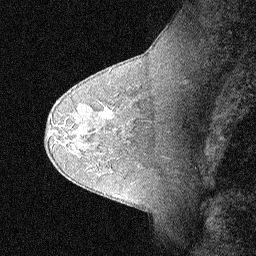
Breast MRI (dynamic contrast-enhanced), one sagittal slice; slice 46 of 64 in the series (ordered by position); dynamic contrast-enhanced study with each time point stored as its own series, time point 2 of 3 at this slice position (early post-contrast, ordered by acquisition time); 1.5 T; TE 4.5 ms, TR 11 ms; 2.06 mm slice thickness; 256 × 256 image matrix, field of view 200 × 200 mm. Female patient, age 62 years. From the clinical record (not read from this slice): setting: breast cancer imaged before/during neoadjuvant chemotherapy; receptor status: HR-positive, HER2-negative.
Annotated regions visible in this slice (semi-automatically segmented with operator editing):
- analysis volume of interest (the breast-tissue region the enhancement analysis was run in; not a lesion): box from (x=91, y=93) to (x=124, y=129) px
- tumour enhancement mask (voxels above the 90 % enhancement threshold inside the analysis volume of interest): (x=100, y=93)–(x=111, y=113)